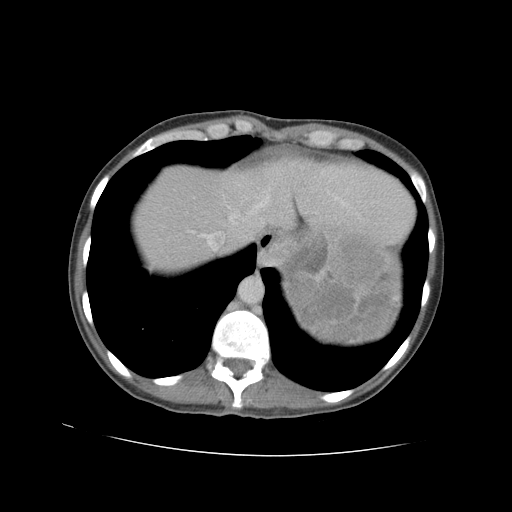
Contrast-enhanced abdominal CT, one axial slice; slice 80 of 90 in the series (ordered by position); reconstruction kernel STANDARD; 120 kVp; soft-tissue window (W 400 / L 40 HU); 5 mm slice thickness; 512 × 512 image matrix. Female patient. From the clinical record (not read from this slice): diagnosis: adrenocortical carcinoma; tumour side: left adrenal; tumour size at pathology: 18 cm; Ki-67 index: 11 %; stage (as recorded): 3.
Outlined on this slice (semi-automatically segmented with operator editing):
- mass: box from (x=283, y=232) to (x=399, y=342) px